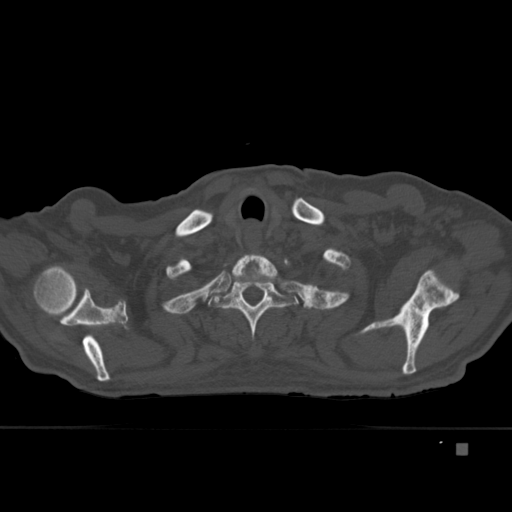
CT including the spine, one axial slice; position 350 of 451 along the scan axis; bone window (W 1800 / L 400 HU); 1.5 mm slice thickness; 512 × 512 image matrix, field of view 378 × 378 mm. Male patient, age 75 years. From the clinical record (not read from this slice): primary cancer: prostate.
Structures marked on this image (semi-automatic segmentation, software-assisted and operator-edited):
- T1 vertebra: bounding box [x1, y1, x2, y2] px = [231, 254, 278, 290]
- T2 vertebra: [203, 261, 299, 340]